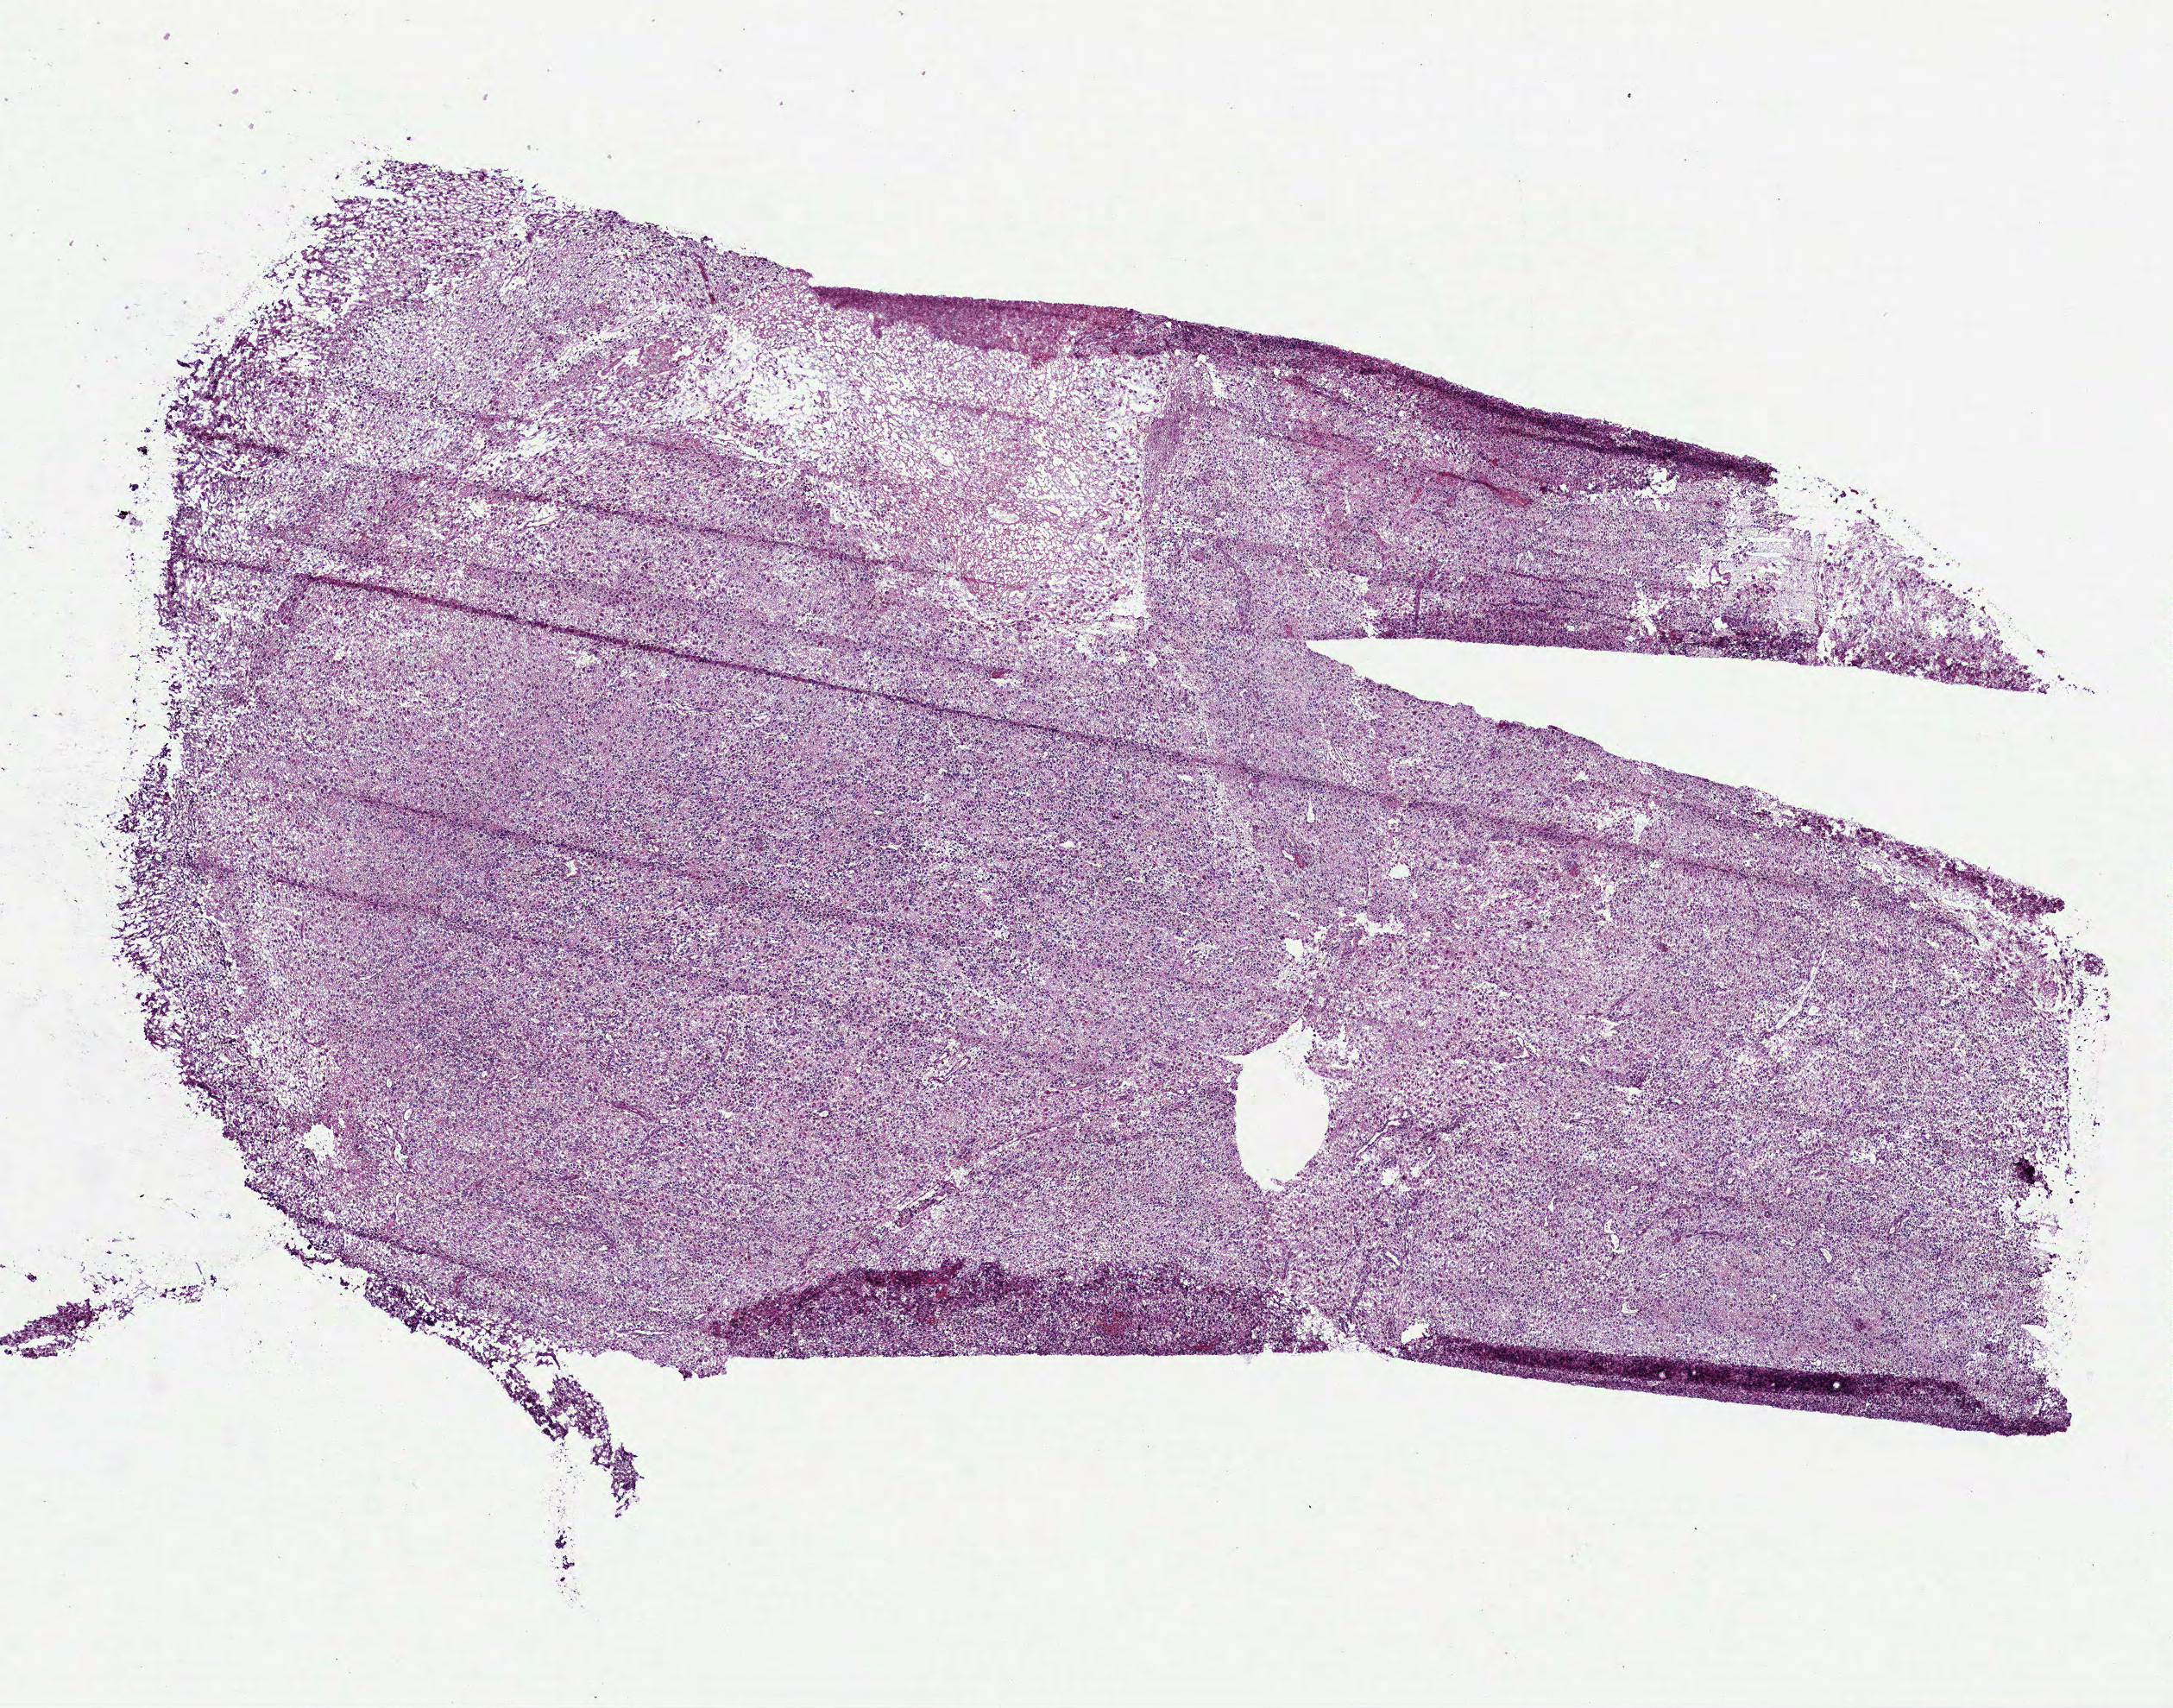
Digitized H&E tissue section (whole slide) — a low-resolution overview of the entire scanned area, about 10.2 x 8.0 mm. Frozen section from the top of the tissue portion. Sample: primary tumour, brain. Patient: male, age at initial diagnosis 33 years. Pathologist review of this section (percent, as recorded): tumour cells 92%, tumour nuclei 85%, normal cells 0%, stromal cells 0%, necrosis 8%.
- diagnosis: Glioblastoma